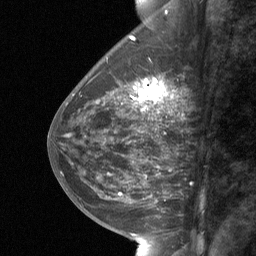
Breast MRI (dynamic contrast-enhanced), one sagittal slice; slice 25 of 64 in the series (ordered by position); dynamic contrast-enhanced study with each time point stored as its own series, time point 2 of 3 at this slice position (early post-contrast, ordered by acquisition time); 1.5 T; TE 4.8 ms, TR 27 ms; 2 mm slice thickness; 256 × 256 image matrix, field of view 180 × 180 mm. Female patient, age 59 years. Case-level facts recorded for this patient, not image findings: setting: breast cancer imaged before/during neoadjuvant chemotherapy; receptor status: triple-negative.
Structures marked on this image (semi-automatically segmented with operator editing):
- analysis volume of interest (the breast-tissue region the enhancement analysis was run in; not a lesion): bounding box (x1, y1, x2, y2) in pixels: (130, 70, 171, 122)
- tumour enhancement mask (voxels above the 90 % enhancement threshold inside the analysis volume of interest): (138, 78, 167, 103)